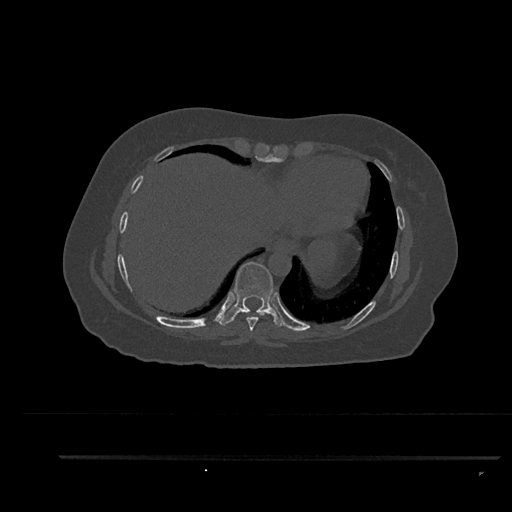
CT including the spine, one axial slice. Slice 432 of 797 in the series (ordered by position). Bone window (W 1800 / L 400 HU). 0.5 mm slice thickness. 512 × 512 image matrix. Female patient, age 44 years. From the clinical record (not read from this slice): primary cancer: renal.
Structures marked on this image (semi-automatic segmentation, software-assisted and operator-edited):
- T8 vertebra: bounding box <241,310,266,331> (left, top, right, bottom; pixels)
- T9 vertebra: <219,262,284,327>